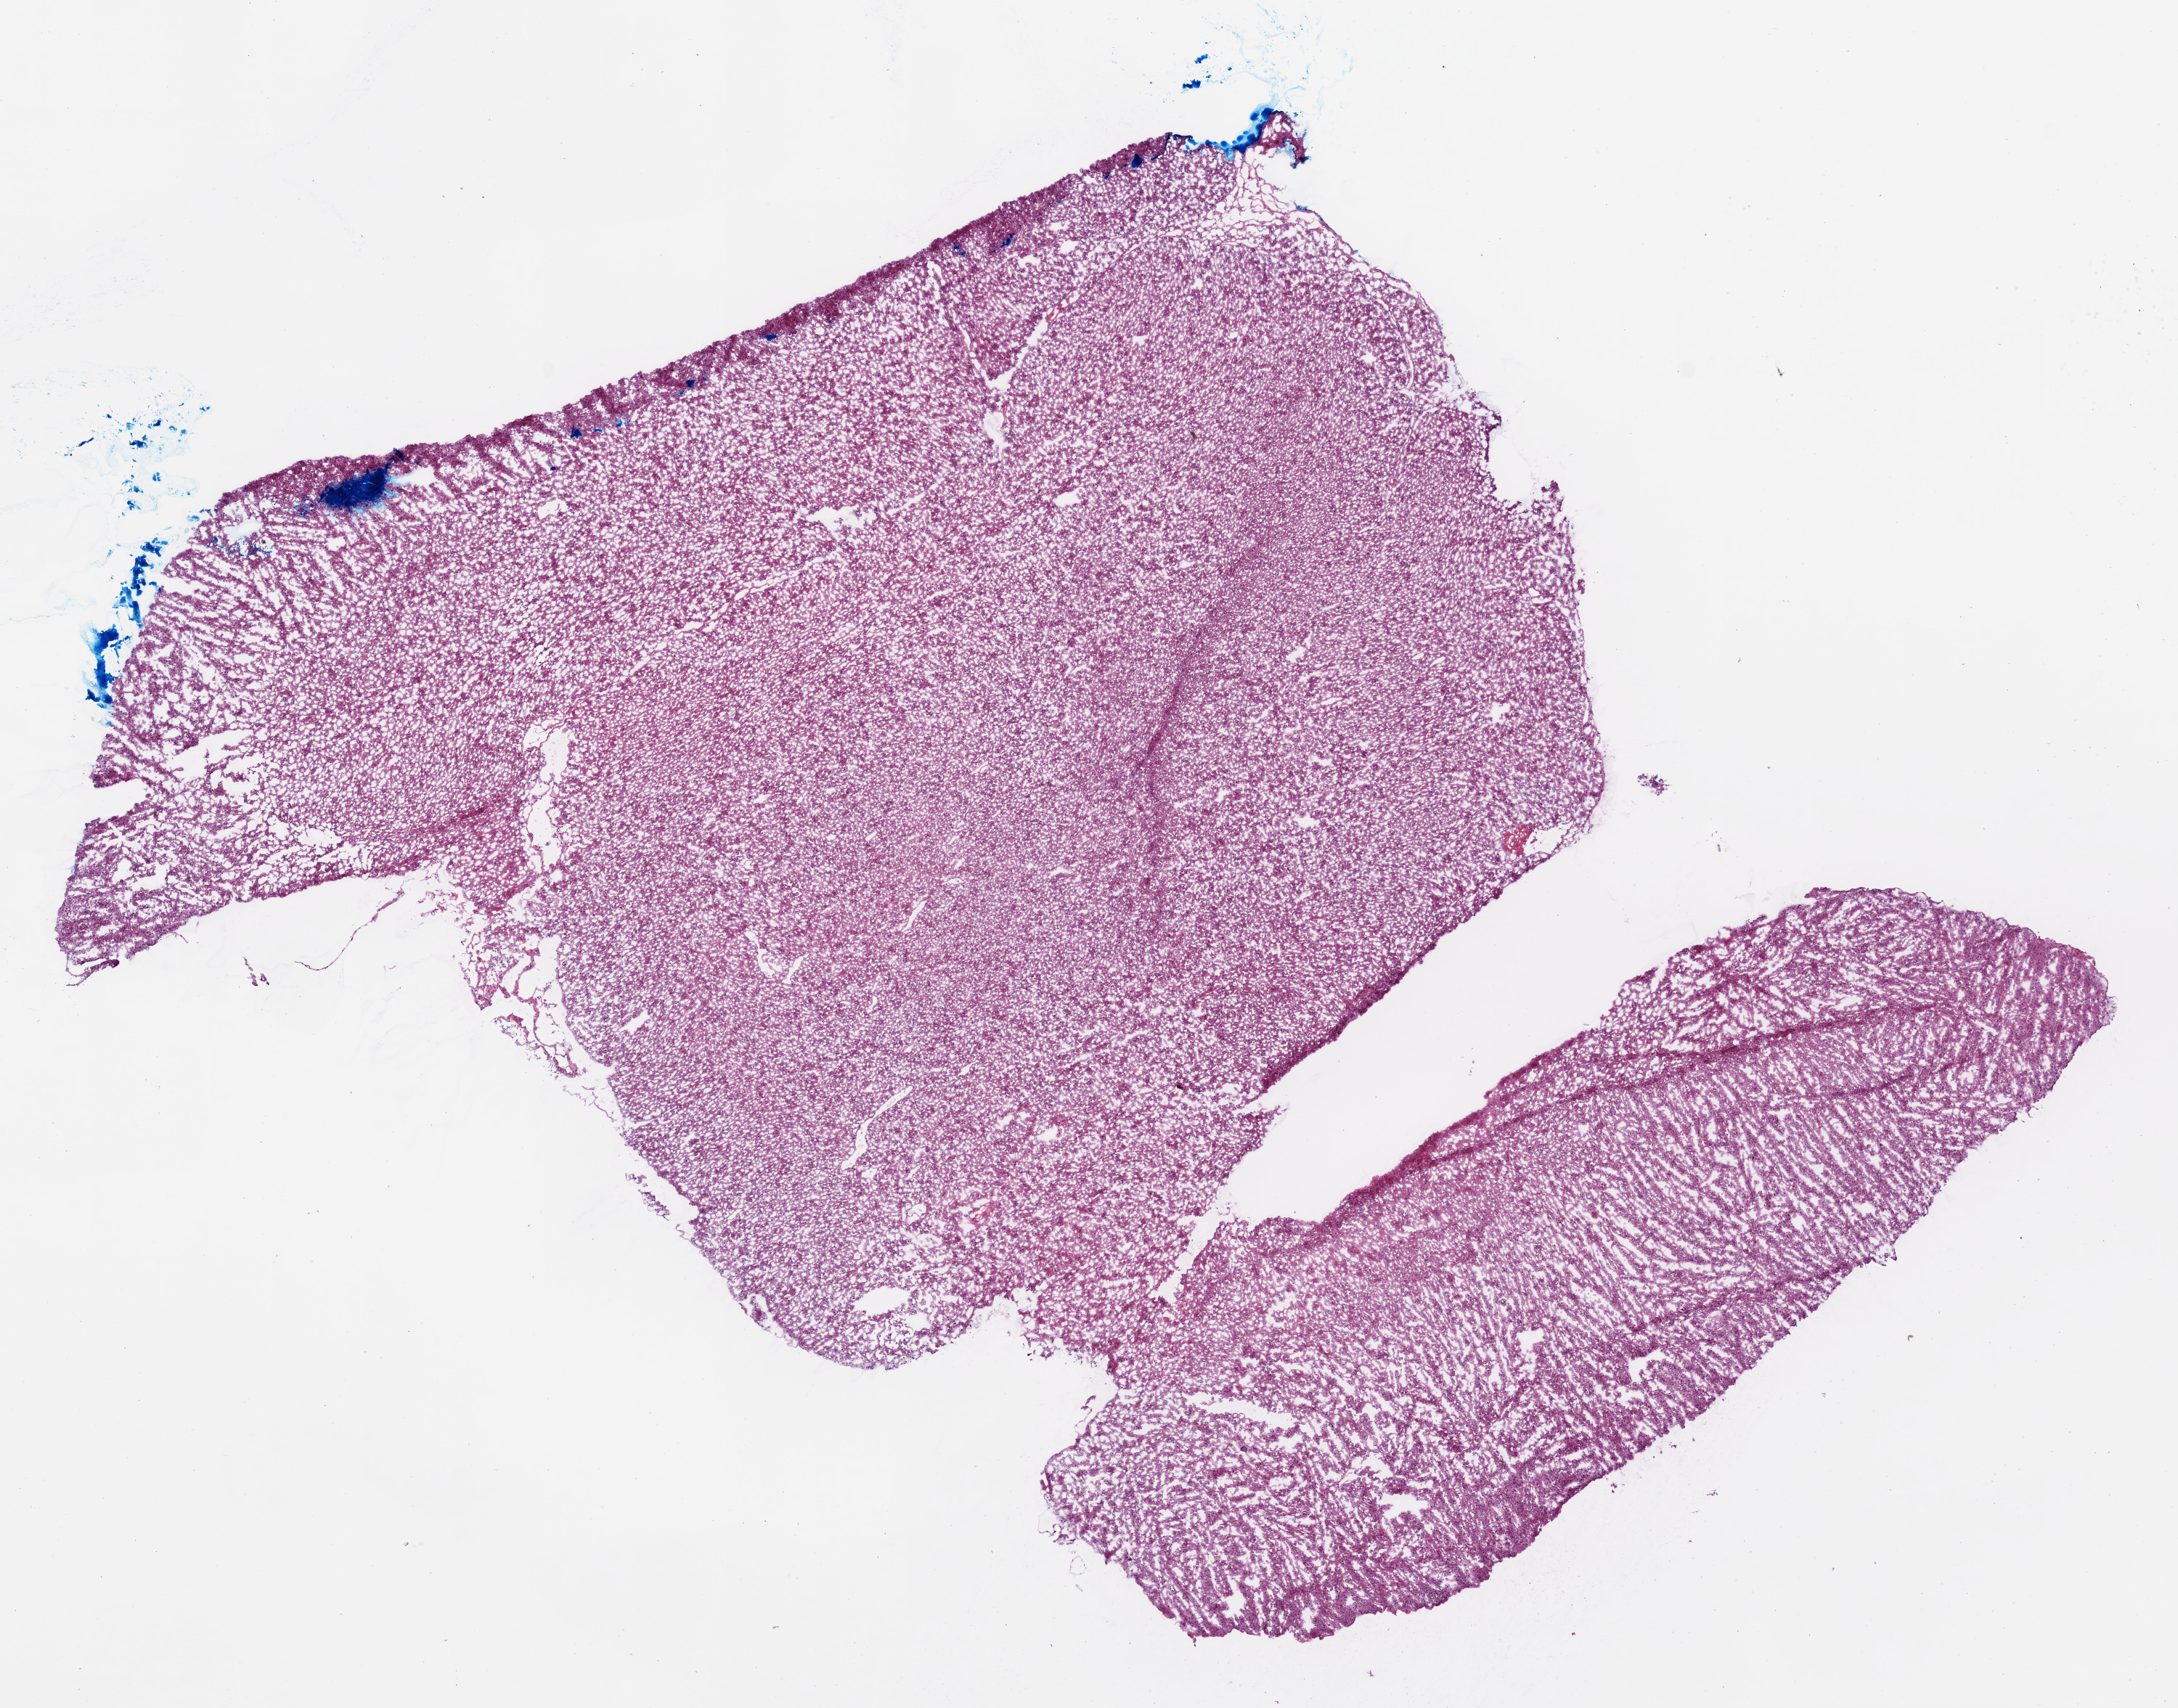
Digitized Hematoxylin and eosin (H&E) stained tissue section (whole slide) — whole scanned area (about 12.0 x 9.4 mm) shown as a low-resolution overview. Frozen section from the bottom of the tissue portion. Primary tumour sample from the brain. Patient: female, age at initial diagnosis 68 years. Slide review estimates, as recorded: tumour cells 100%, tumour nuclei 85%, normal cells 0%, stromal cells 0%, necrosis 0%.
Pathologic diagnosis: Glioblastoma.